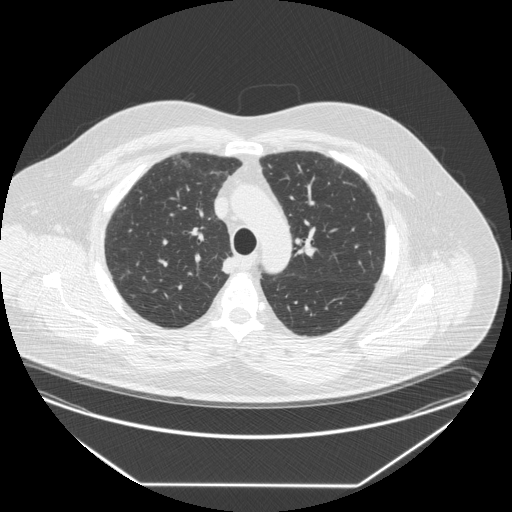
Axial slice from a low-dose chest CT screening exam; third annual screen; lung window (W 1500 / L -600 HU); slice 59 of 258 in the series; 512 × 512 image matrix. Male participant, aged 58 years at enrolment. Former smoker at enrolment.
Lesion marked by an expert reader, box from (x=214, y=253) to (x=246, y=282) px. Screening reader's record for this exam (one nodule recorded; not confirmed to be the boxed lesion): non-calcified nodule or mass ≥4 mm, right upper lobe, 15 × 12 mm, smooth margins, soft tissue attenuation, pre-existing on the prior screen: no.